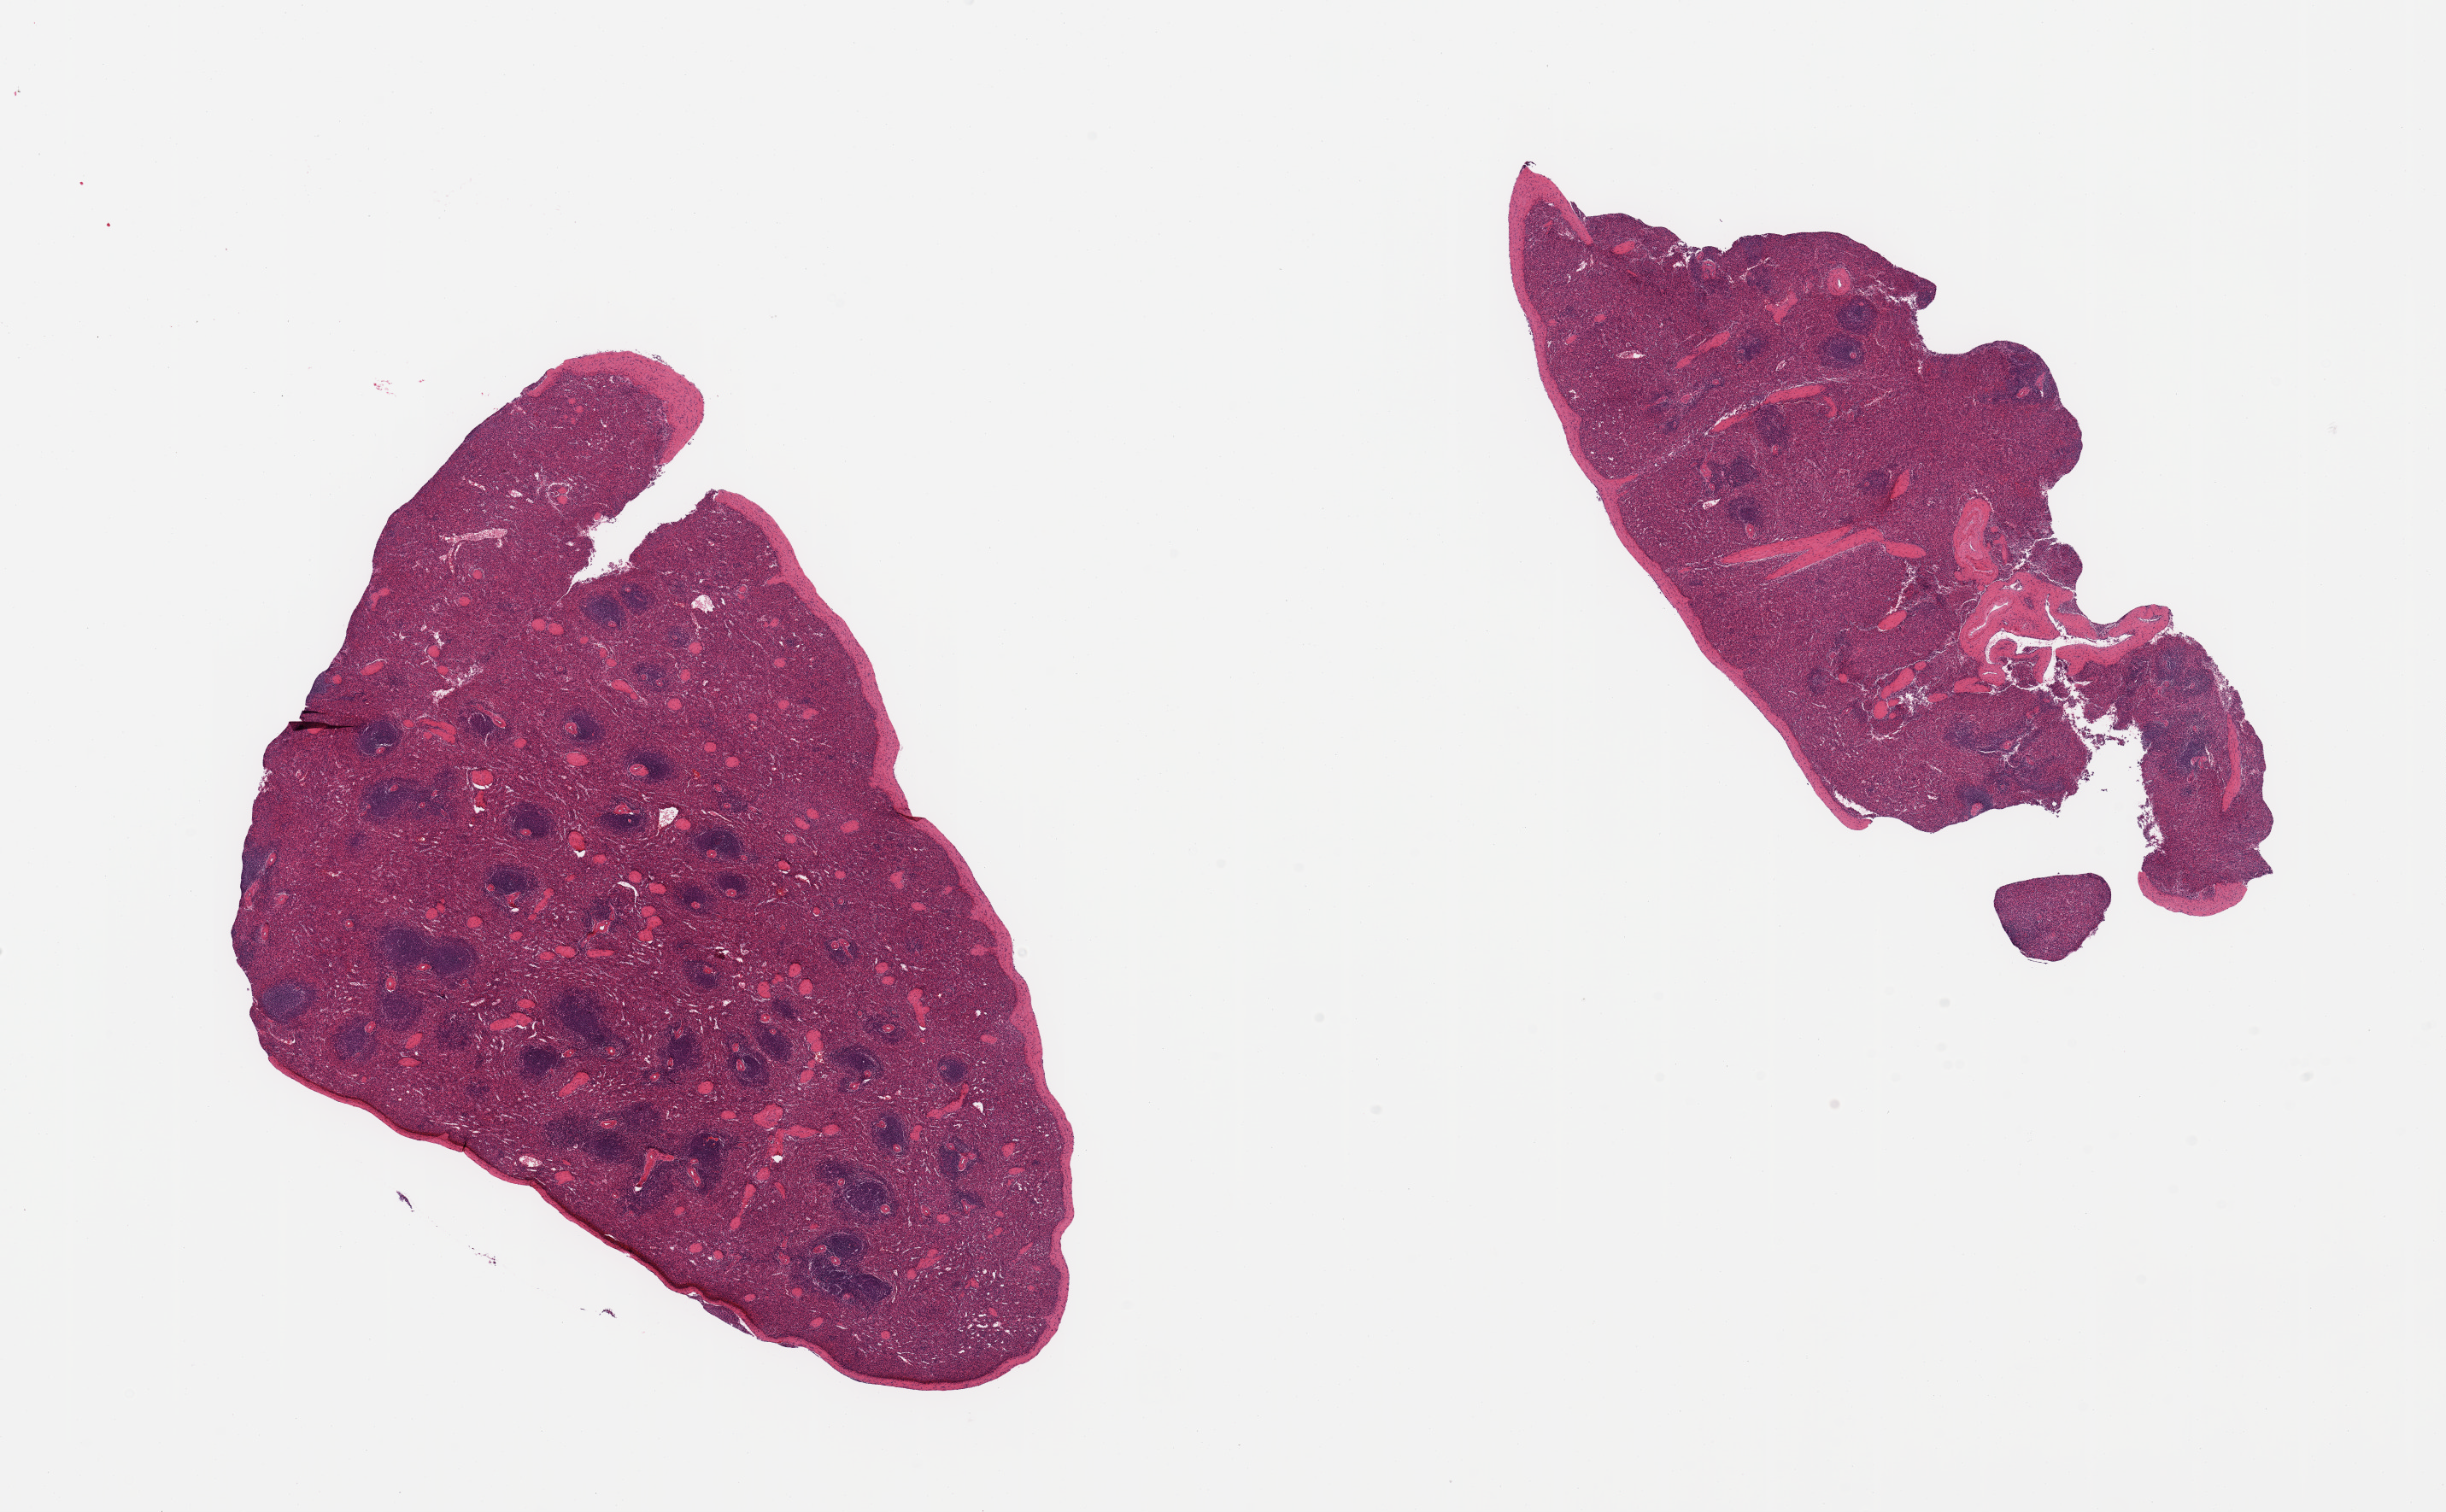
H&E whole-slide image — low-resolution overview of the scanned area, about 22.6 x 14.0 mm. PAXgene-fixed, paraffin-embedded tissue. Sampled site (target tissue): spleen. Tissue donor sample. Donor: male.
Reviewer comment on this tissue sample: 2 pieces, no abnormalities.